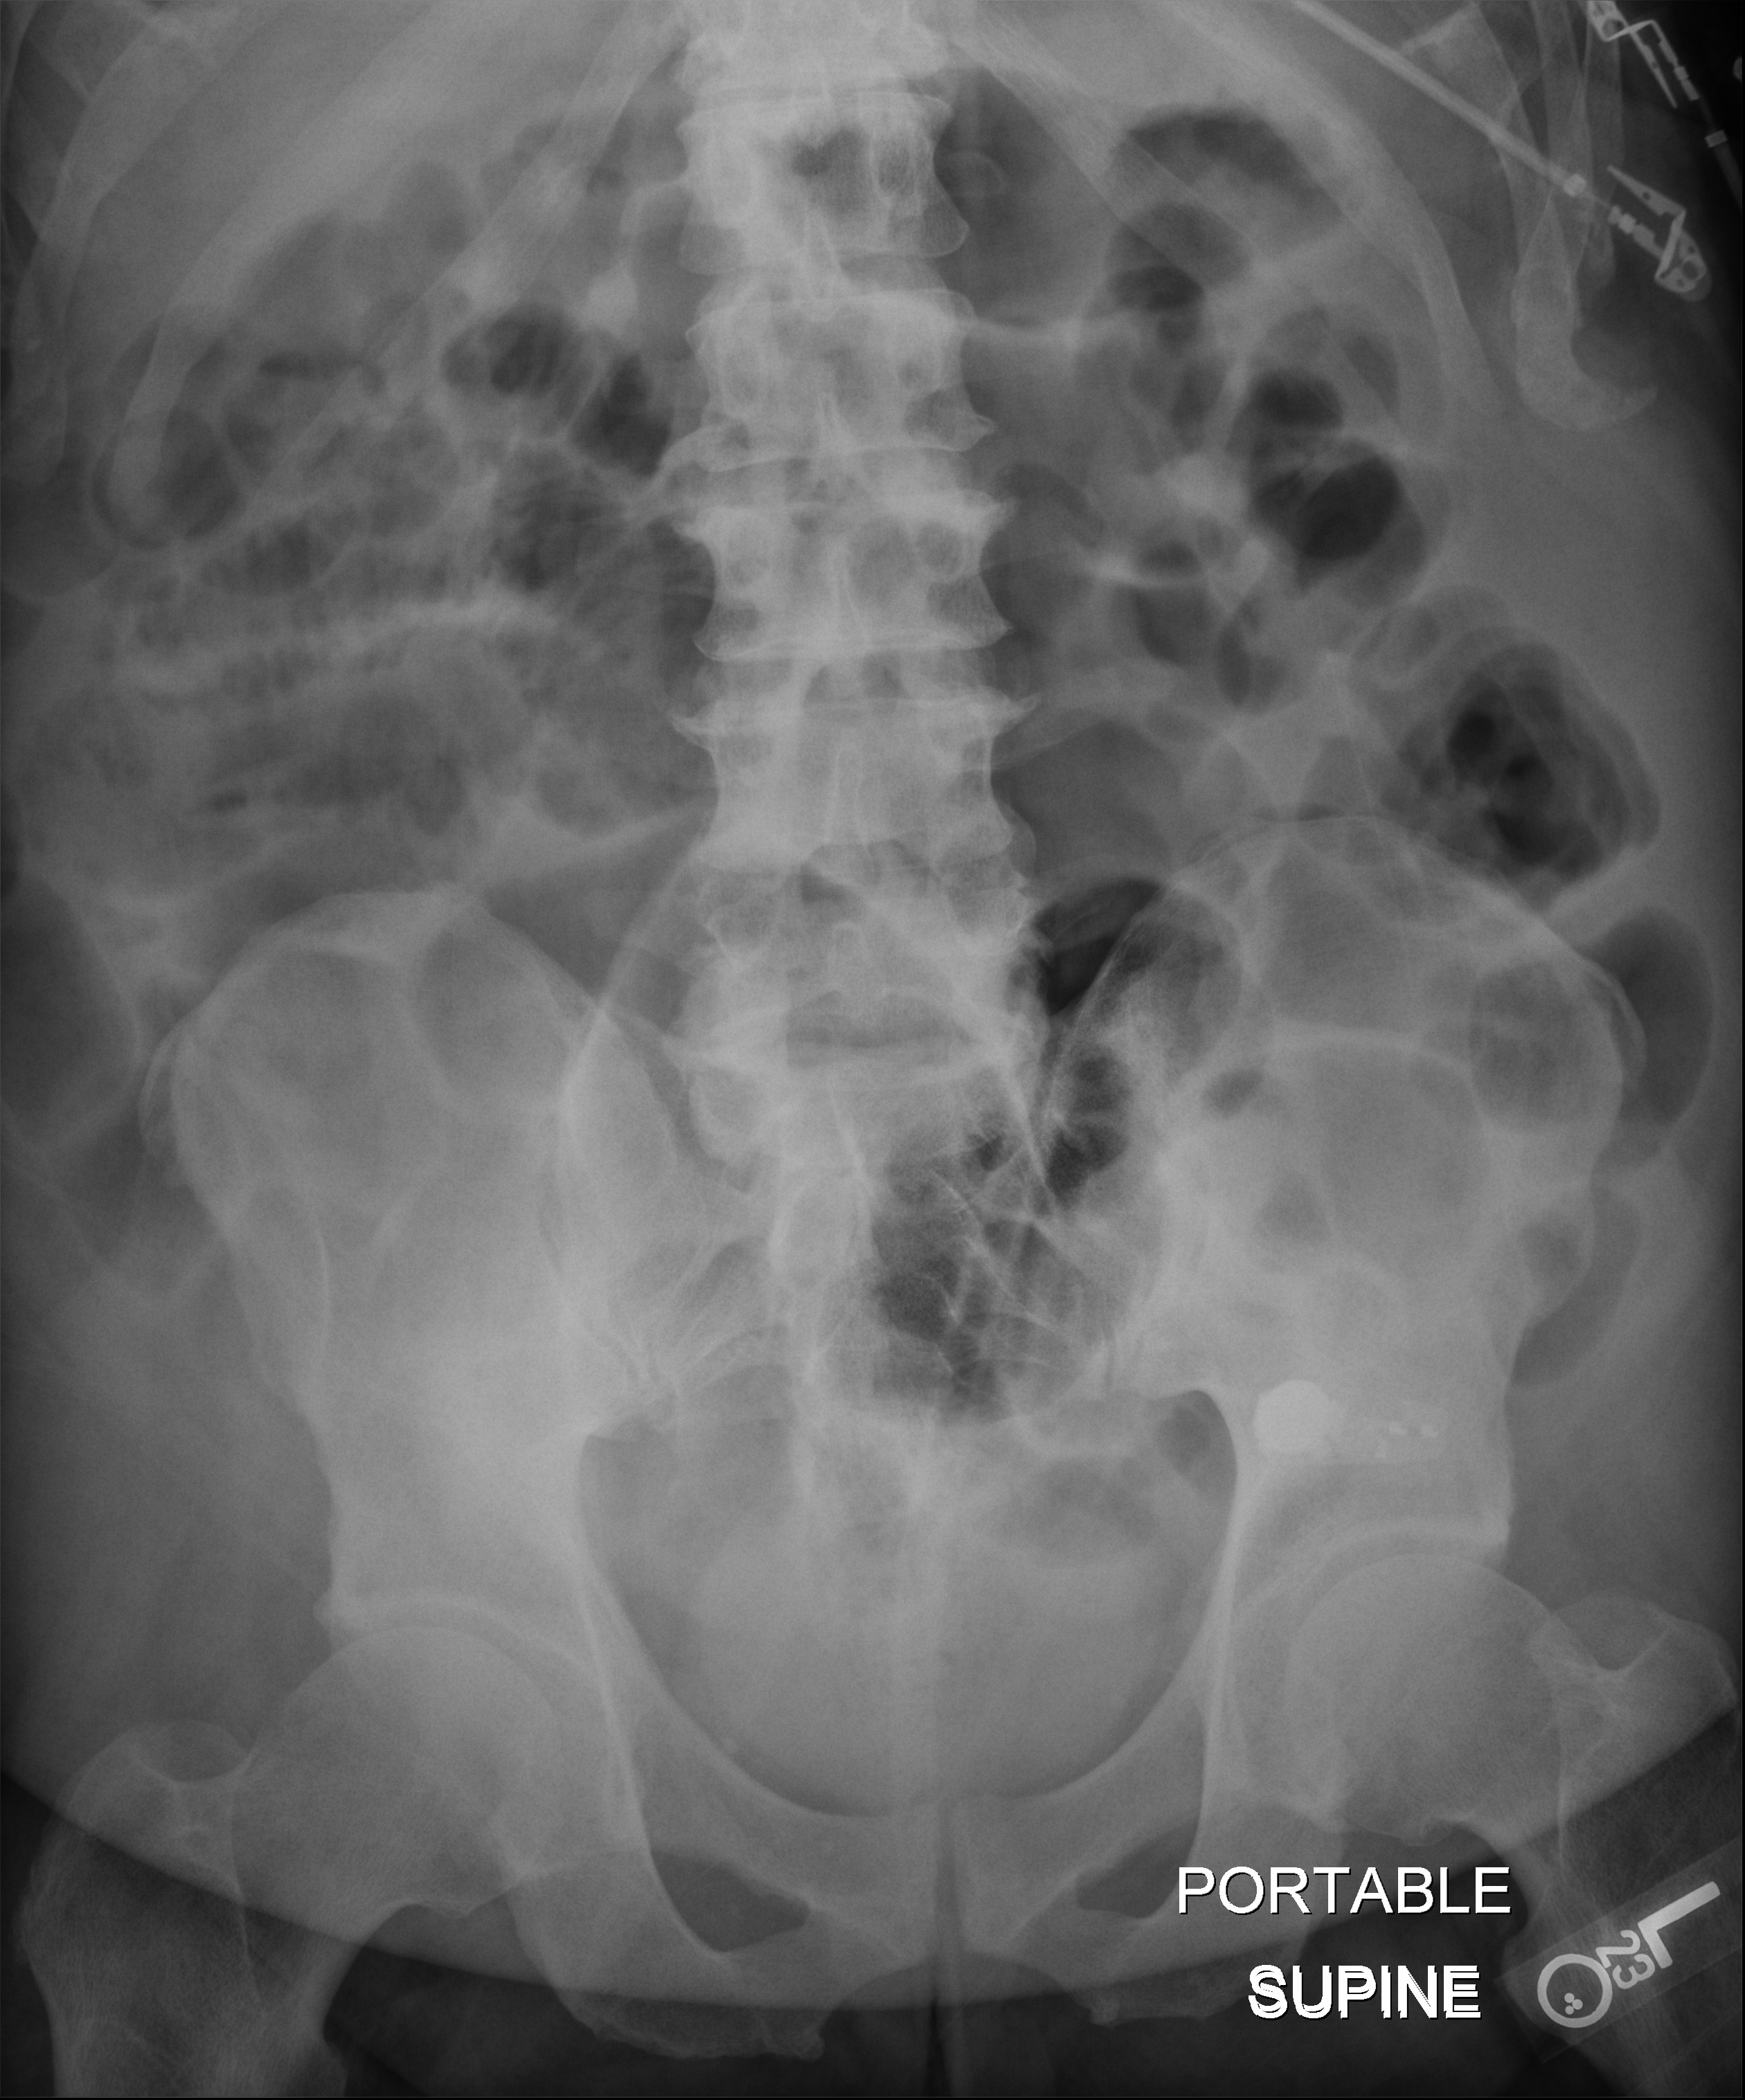
Abdomen X-ray (portable). Male patient hospitalised with COVID-19, age 18–59 years.
Admission-level facts for this patient (not findings on this image; timing relative to this image not recorded): length of hospital stay: 41 days.